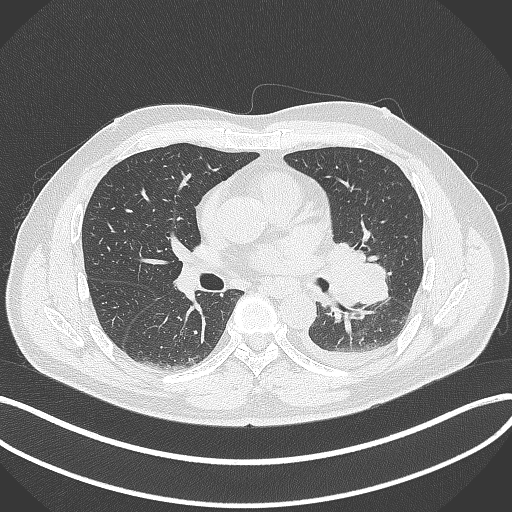
Chest CT, one axial slice. Slice 190 of 342 in the series (ordered by position). 120 kVp. Lung window (W 1500 / L -600 HU). 1 mm slice thickness. 512 × 512 image matrix, field of view 400 × 400 mm. Patient: male, 58 years. From the clinical record (not read from this slice): clinical TNM (as recorded): T3 N1 M1b.
Structures marked on this image (rectangle marked by the reading radiologist):
- lung tumour (recorded histology: small cell carcinoma): bounding box (x1, y1, x2, y2) in pixels: (323, 237, 390, 309)